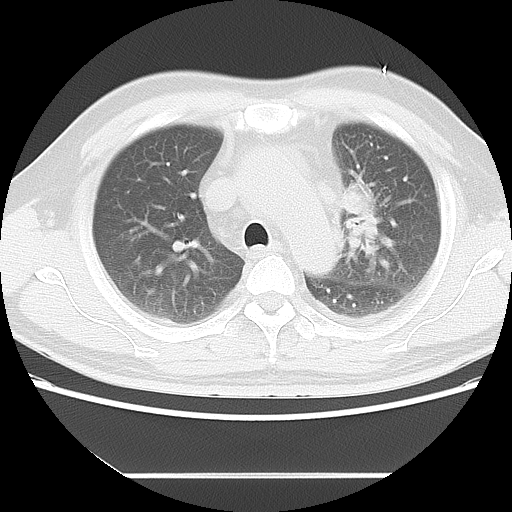
Chest CT, one axial slice. 120 kVp. Lung window (W 1500 / L -600 HU). 512 × 512 image matrix, field of view 350 × 350 mm. Patient: male, 56 years. Case-level facts recorded for this patient, not image findings: clinical TNM (as recorded): T2 N3 M1.
Outlined on this slice (rectangle marked by the reading radiologist):
- lung tumour (recorded histology: adenocarcinoma): bounding box (x1, y1, x2, y2) in pixels: (345, 177, 387, 231)